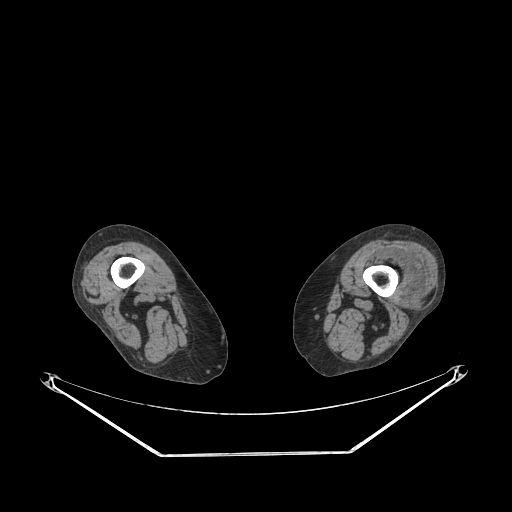
CT of an extremity soft-tissue mass (from a PET/CT study), one axial slice. Position 194 of 267 along the scan axis. 140 kVp. Soft-tissue window (W 400 / L 40 HU). 512 × 512 image matrix, field of view 500 × 500 mm. Female patient. From the clinical record (not read from this slice): histological type: undifferentiated – high grade; grade: high; site of the primary tumour: left thigh.
Annotated regions visible in this slice (expert contour drawn on MRI and transferred to this co-registered scan by the dataset authors):
- gross tumour volume including surrounding oedema: bounding box (x1, y1, x2, y2) in pixels: (375, 253, 428, 296)